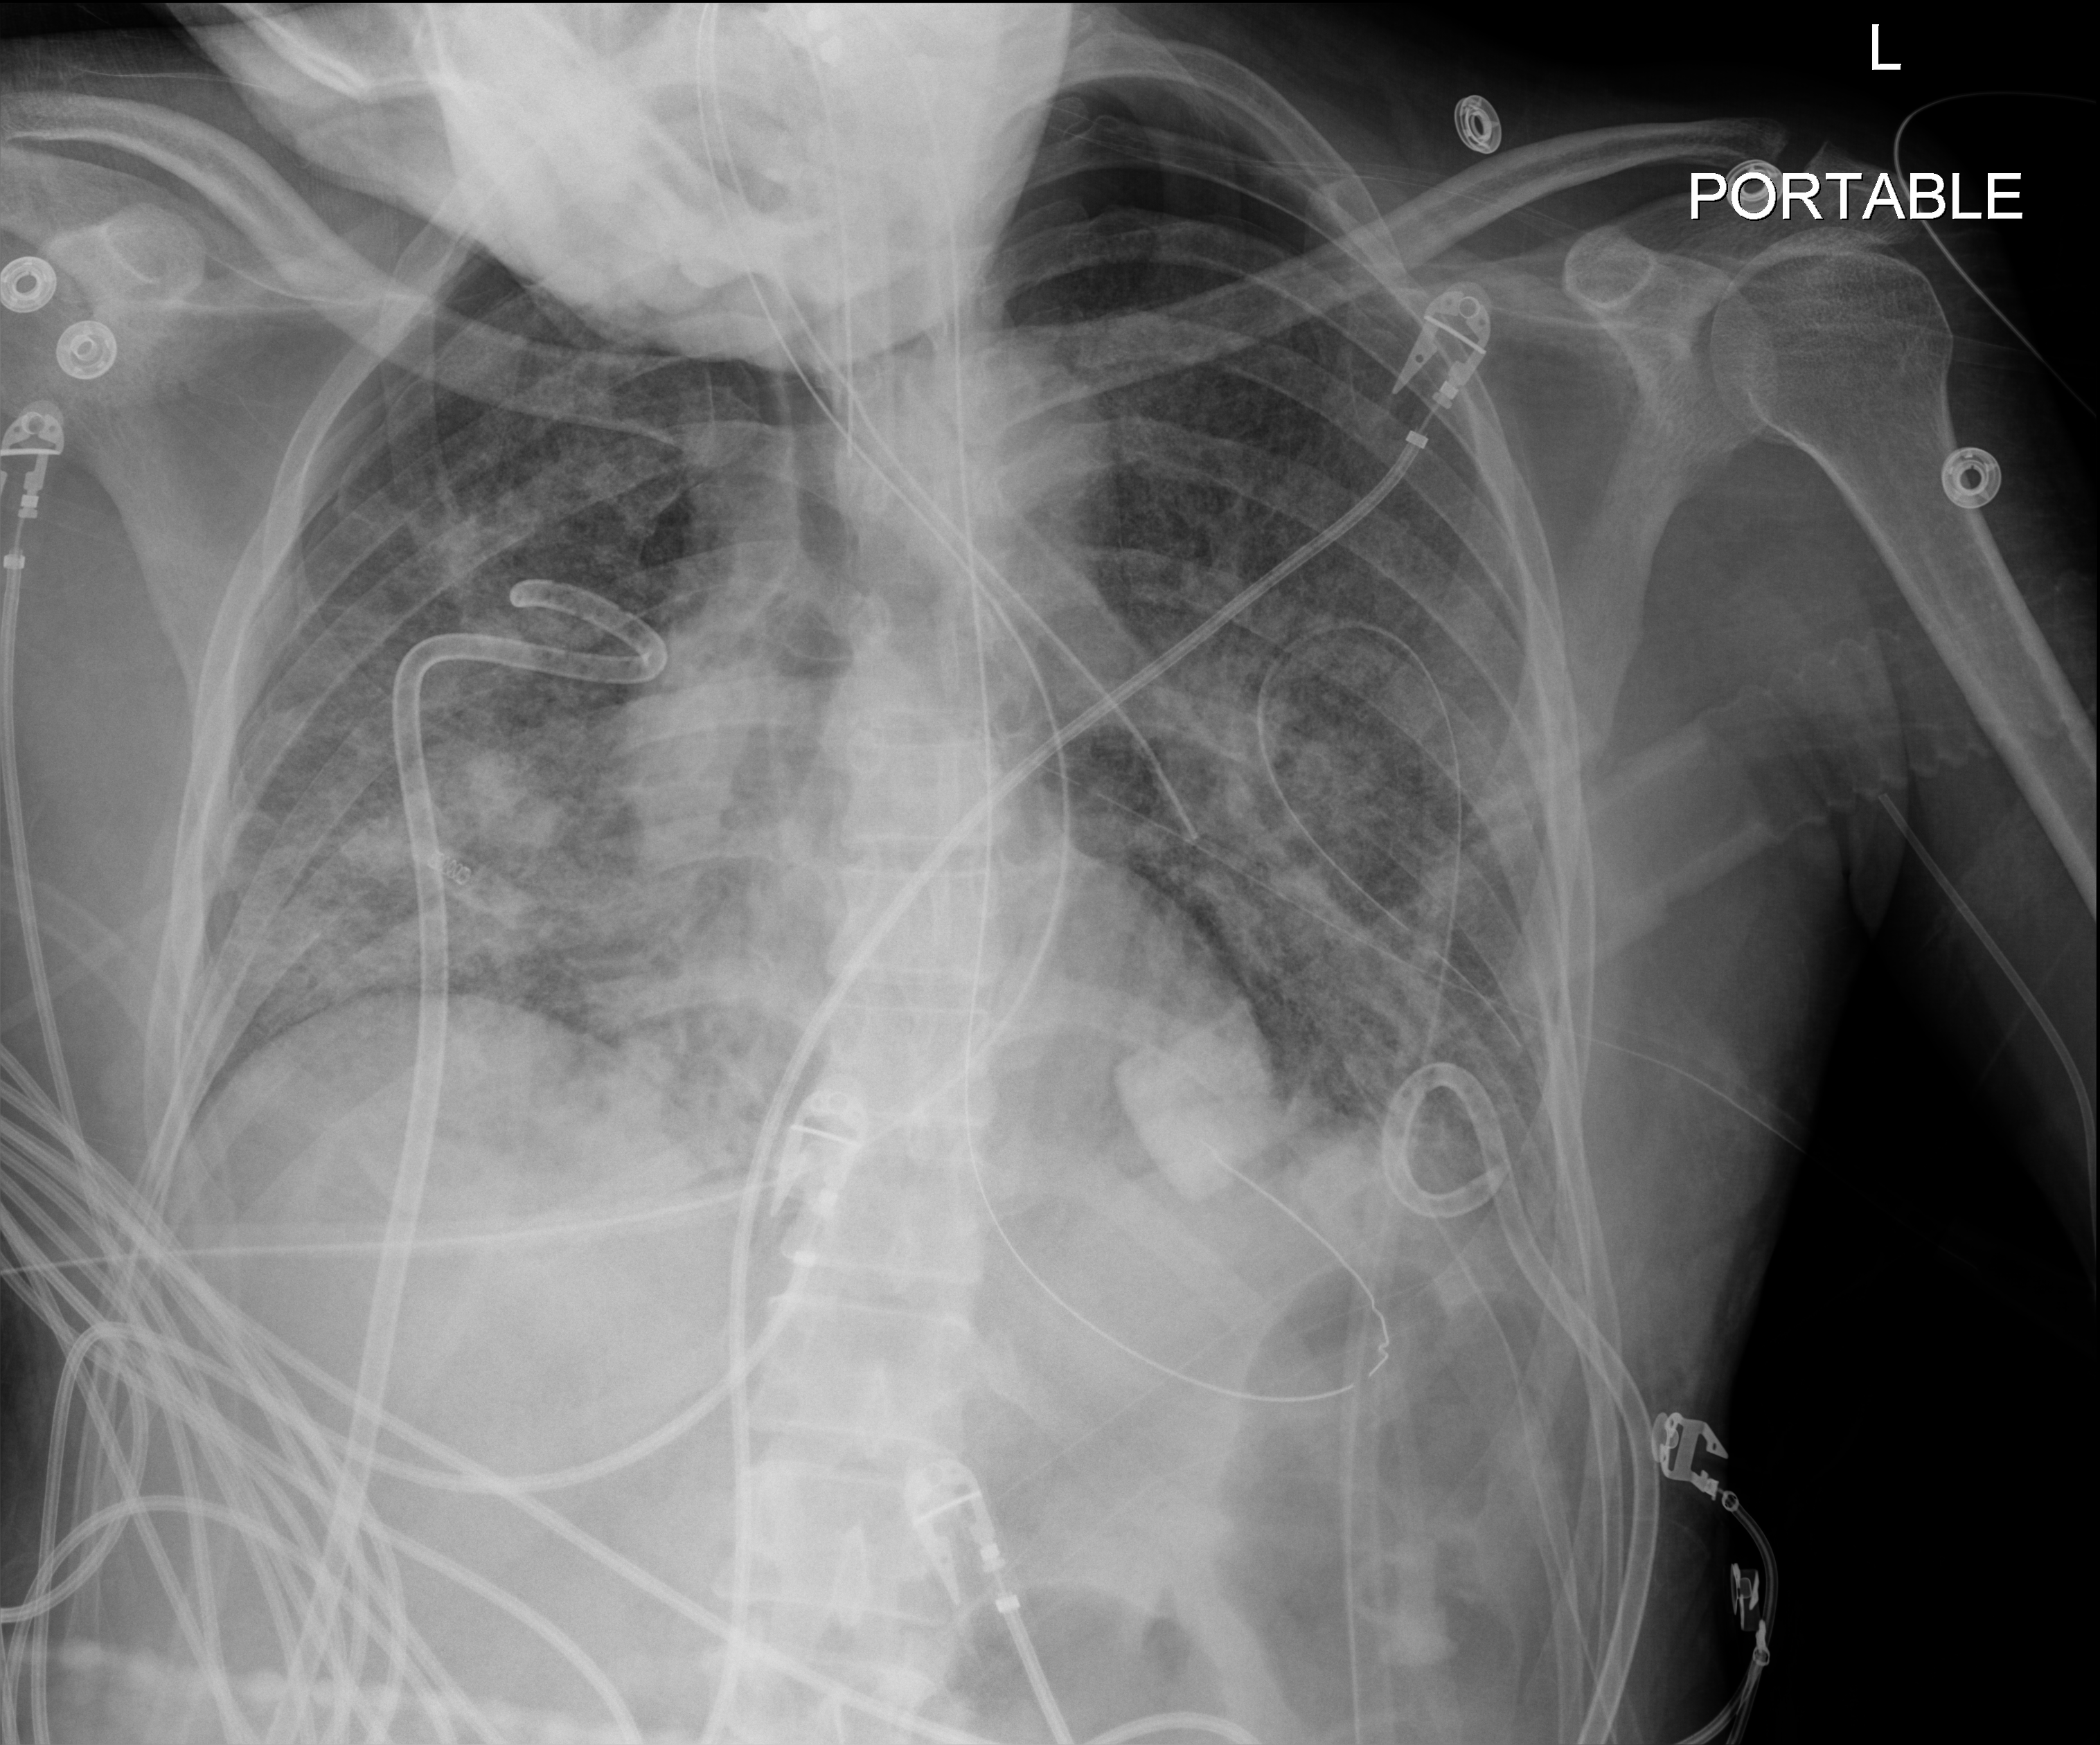
Chest X-ray (portable); anteroposterior (AP) projection. Adult patient hospitalised with COVID-19, age 18–59 years.
Hospital-stay facts (about this admission, not read from this image; timing relative to this image not recorded): length of hospital stay: 41 days; admitted to intensive care during this hospital stay: yes; mechanically ventilated during this hospital stay: yes.